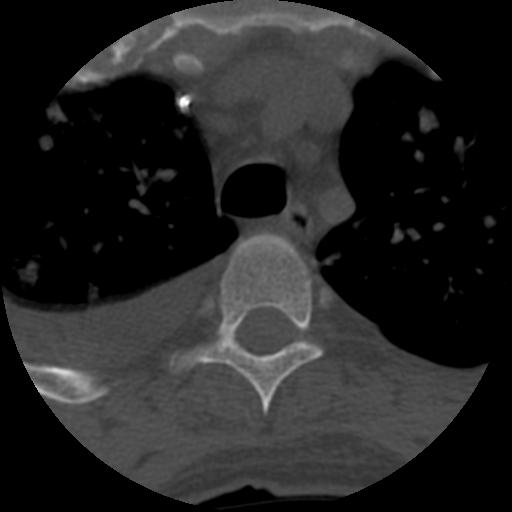
CT including the spine, one axial slice. Position 472 of 708 along the scan axis. Reconstruction kernel STANDARD. 120 kVp. One of 3 acquisitions stored at this slice position. Bone window (W 1800 / L 400 HU). 1.25 mm slice thickness. 512 × 512 image matrix. Patient age 55 years. From the clinical record (not read from this slice): primary cancer: colon.
Structures marked on this image (semi-automatically segmented with operator editing):
- T4 vertebra: bounding box (x1, y1, x2, y2) in pixels: (170, 235, 321, 415)